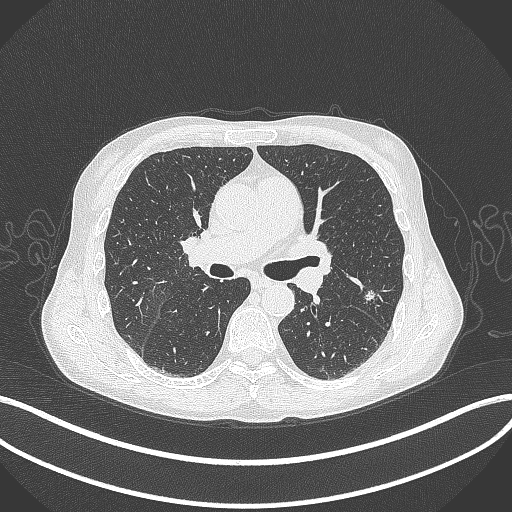
Chest CT, one axial slice. Slice 213 of 429 in the series (ordered by position). 120 kVp. Lung window (W 1500 / L -600 HU). 1 mm slice thickness. 512 × 512 image matrix. Male patient, age 58 years. Case-level facts recorded for this patient, not image findings: clinical TNM (as recorded): T1c N0 M0; histopathological grade: G2.
Annotated regions visible in this slice (bounding box drawn by a radiologist):
- lung tumour (recorded histology: adenocarcinoma): bounding box [x1, y1, x2, y2] px = [362, 286, 378, 306]